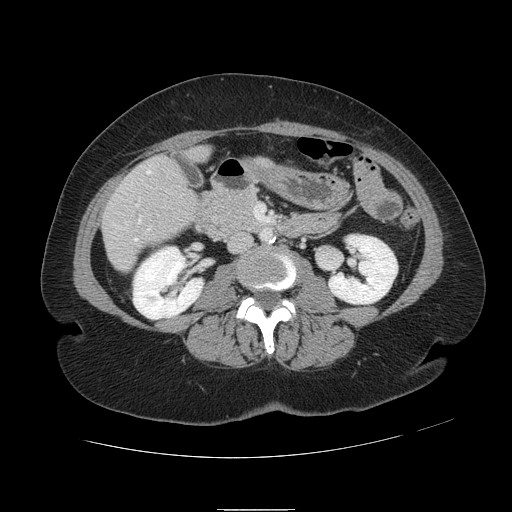
Contrast-enhanced abdominal CT, one axial slice; position 26 of 121 along the scan axis; 120 kVp; soft-tissue window (W 400 / L 40 HU); 2.5 mm slice thickness; 512 × 512 image matrix. Female patient, age 52 years. Case-level facts recorded for this patient, not image findings: diagnosis: colorectal cancer liver metastases, imaged before liver resection; multiple liver metastases: yes; largest metastasis: 6.3 cm; disease in both lobes: no.
Annotated regions visible in this slice (expert manual segmentation):
- hepatic veins: bounding box [x1, y1, x2, y2] px = [135, 171, 151, 241]
- liver: [103, 148, 210, 271]
- planned liver remnant (the part of the liver to remain after resection): [191, 148, 210, 161]
- portal vein (with intrahepatic branches): [136, 205, 139, 207]